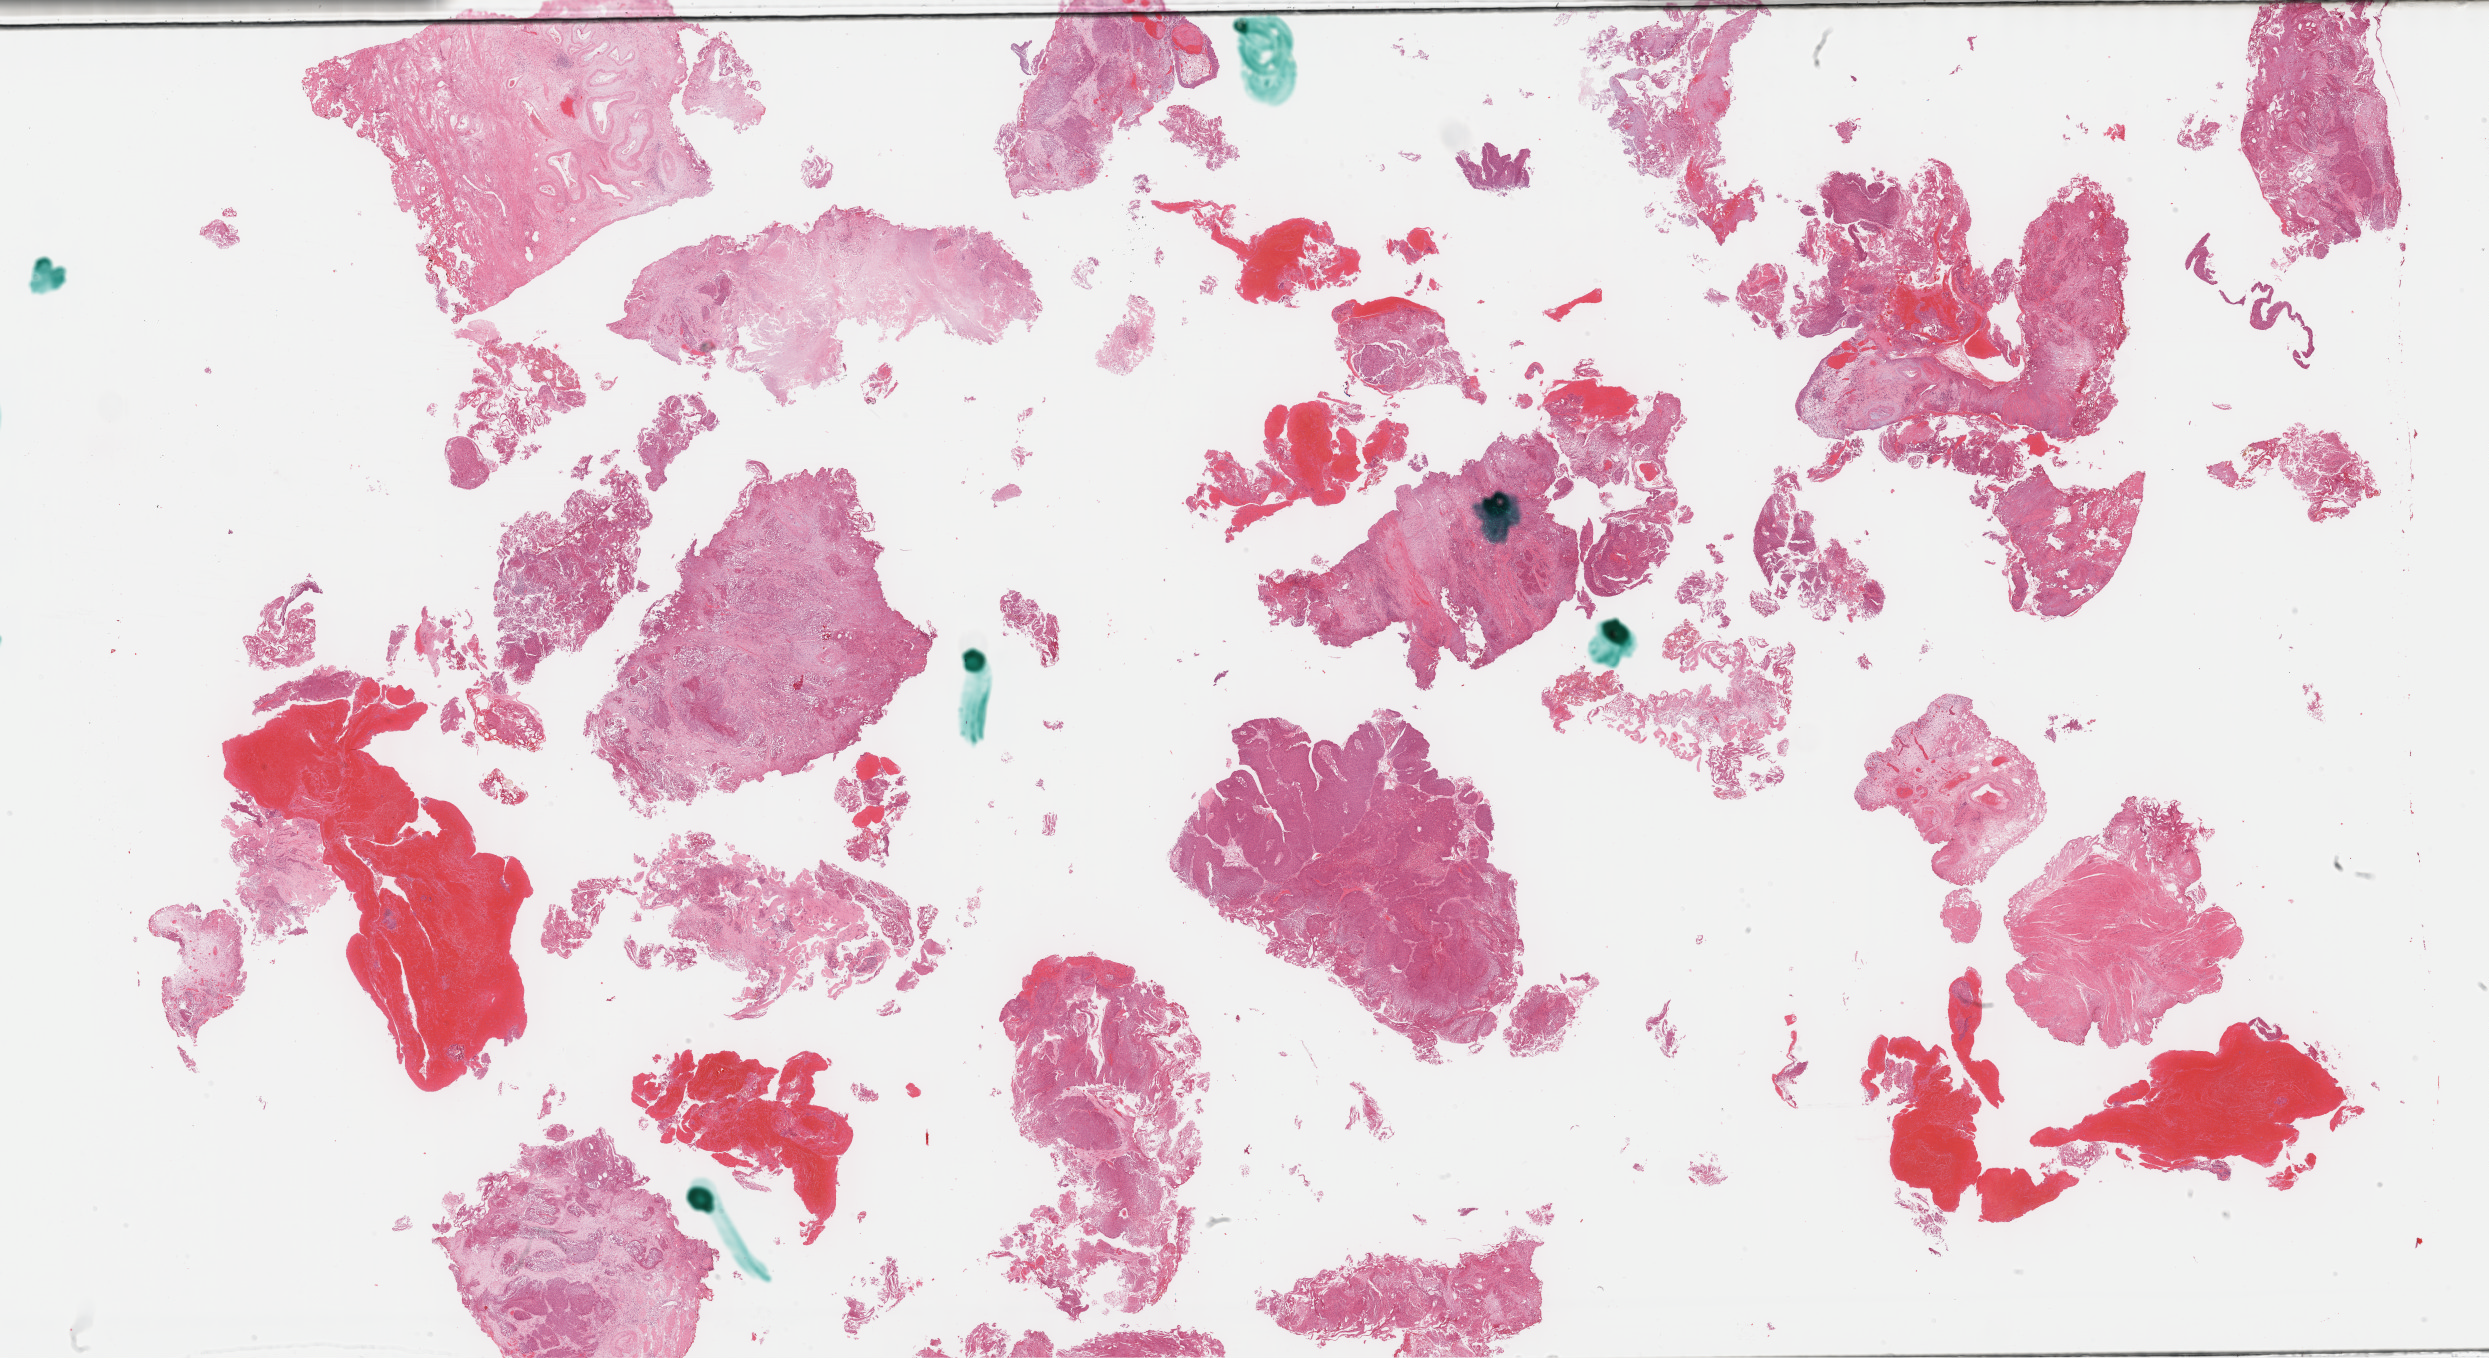
Whole-slide histology image, Hematoxylin and eosin (H&E) stained — whole scanned area (about 40.3 x 22.0 mm) shown as a low-resolution overview; formalin-fixed paraffin-embedded (FFPE) diagnostic section; sample: primary tumour, bladder. Patient: female, age at initial diagnosis 78 years. Histologic grade: high grade.
Diagnosis: Transitional cell carcinoma. AJCC pathologic stage: II.